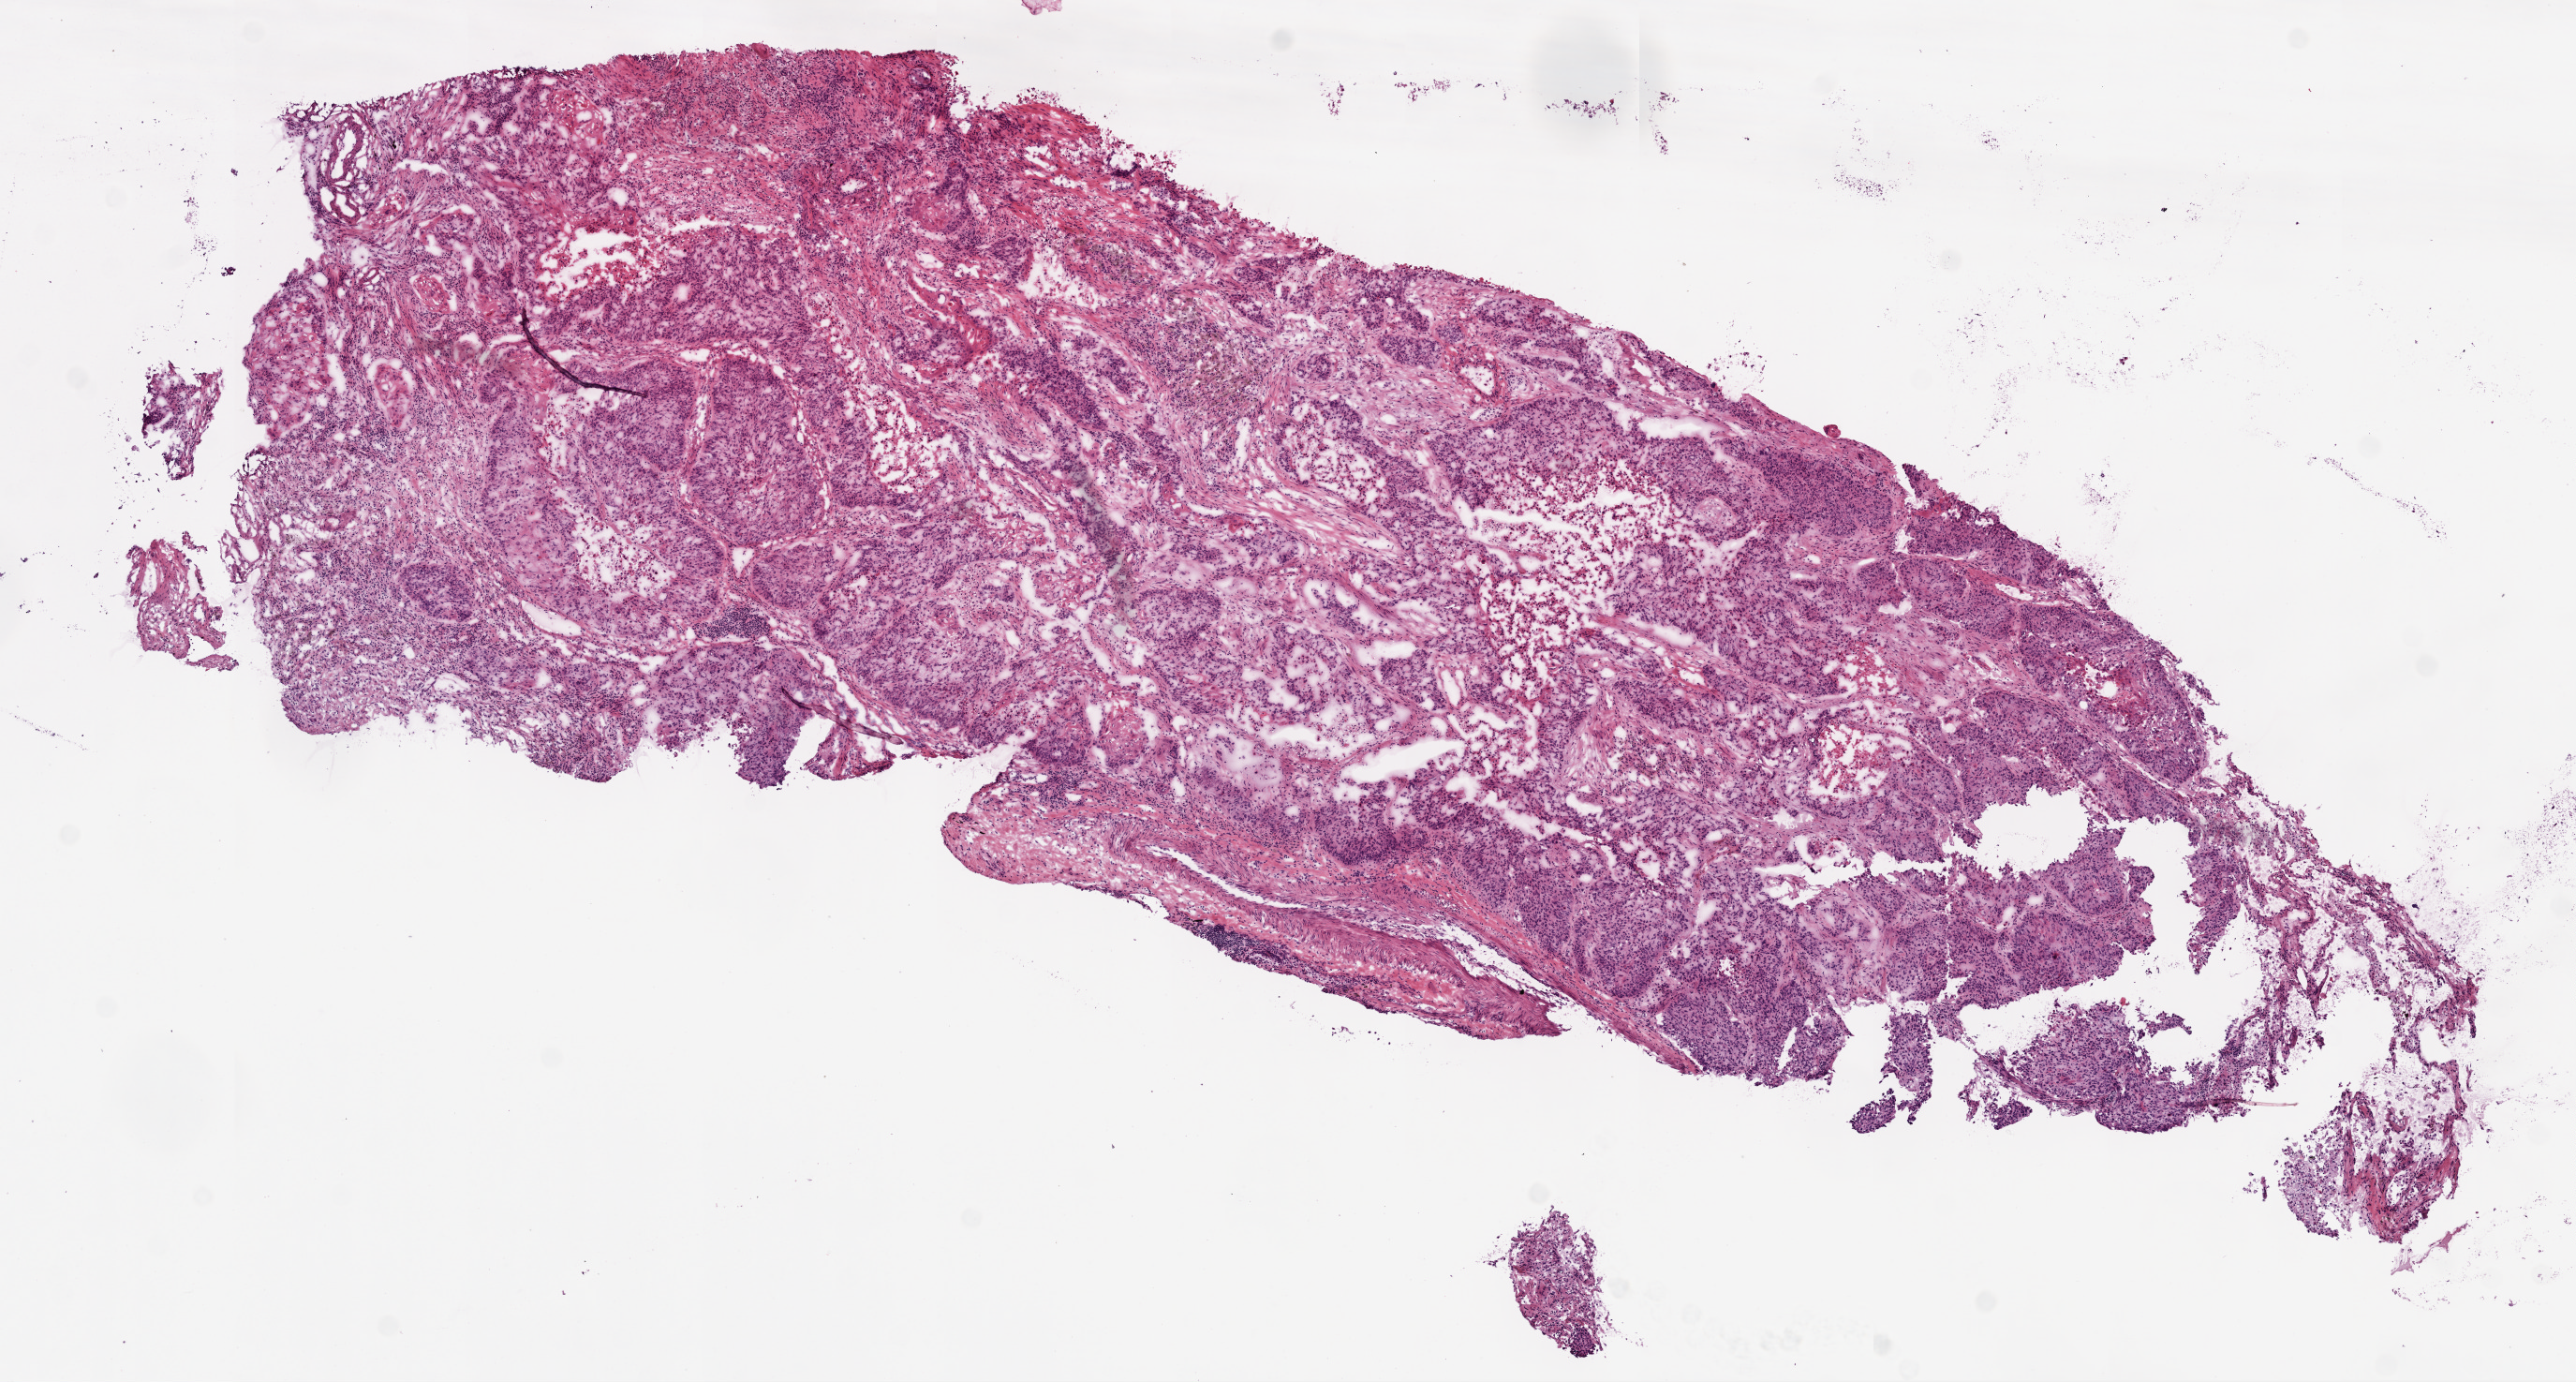
Digitized H&E-stained tissue section (whole slide) — low-resolution overview of the scanned area, about 11.0 x 5.9 mm (acquisition: 20x scan), frozen section from the top of the tissue portion, lung, primary tumour sample. Male patient; age at initial diagnosis 55 years. Pathologist review of this section (percent, as recorded): tumour cells 80%, tumour nuclei 65%, normal cells 0%, stromal cells 15%, necrosis 5%.
Diagnosis: Squamous cell carcinoma, NOS (lower lobe, lung). AJCC pathologic stage: IA. TNM: T1 N0 M0.